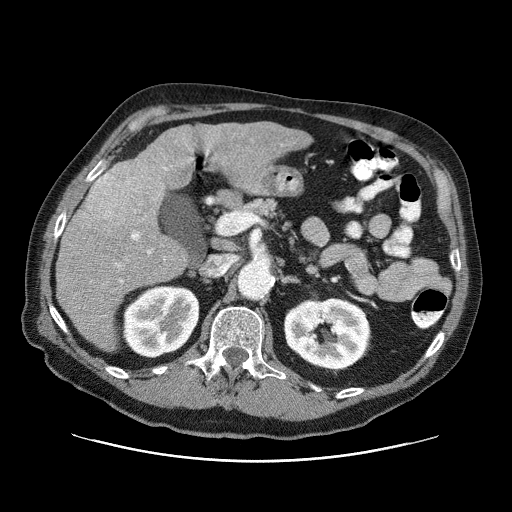
Contrast-enhanced abdominal CT (liver protocol), one axial slice. Slice 34 of 87 in the series (ordered by position). One of 3 acquisitions stored at this slice position. Soft-tissue window (W 400 / L 40 HU). 2.5 mm slice thickness. 512 × 512 image matrix. From the clinical record (not read from this slice): diagnosis: hepatocellular carcinoma (patient treated with transarterial chemoembolisation; whether this scan precedes or follows treatment is not stated here); TNM stage (as recorded): Stage-IIIA; Child-Pugh class: A; tumour differentiation: well differentiated; tumour nodularity: multinodular.
Structures marked on this image (semi-automatic segmentation, software-assisted and operator-edited):
- liver parenchyma outside the tumour (the mass and vessels are separate outlines, so this box may not span the whole liver): bounding box [x1, y1, x2, y2] px = [56, 122, 312, 350]
- mass: [74, 153, 164, 231]
- liver vessels: [116, 151, 208, 283]